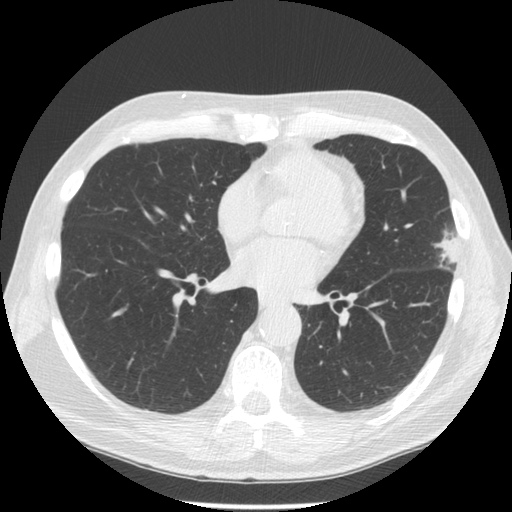
Low-dose screening chest CT, one axial slice; position 65 of 134 along the scan axis; reconstruction kernel STANDARD; 120 kVp; lung window (W 1500 / L -600 HU); 512 × 512 image matrix, field of view 350 × 350 mm.
Structures marked on this image (outlined manually by an expert reader):
- lesion 1 (tumor, upper lobe of left lung): bounding box (x1, y1, x2, y2) in pixels: (435, 230, 459, 267)